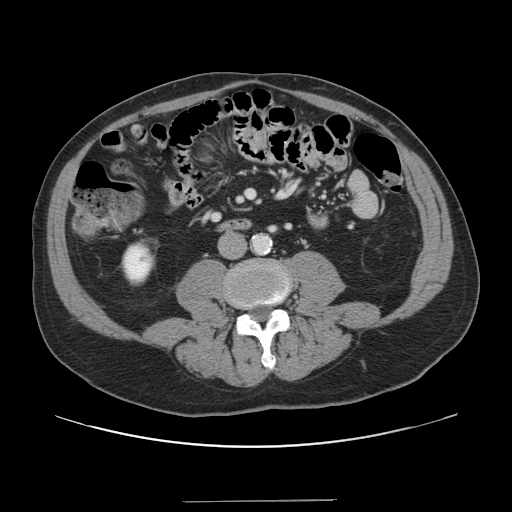
Contrast-enhanced abdominal CT, one axial slice; position 17 of 151 along the scan axis; 120 kVp; intravenous contrast given; soft-tissue window (W 400 / L 40 HU); 2.5 mm slice thickness; 512 × 512 image matrix. Male patient, age 63 years. From the clinical record (not read from this slice): diagnosis: colorectal cancer liver metastases, imaged before liver resection; multiple liver metastases: no; largest metastasis: 2.1 cm.
Outlined on this slice (manually delineated by an expert):
- portal vein (with intrahepatic branches): bounding box [x1, y1, x2, y2] px = [248, 192, 253, 198]